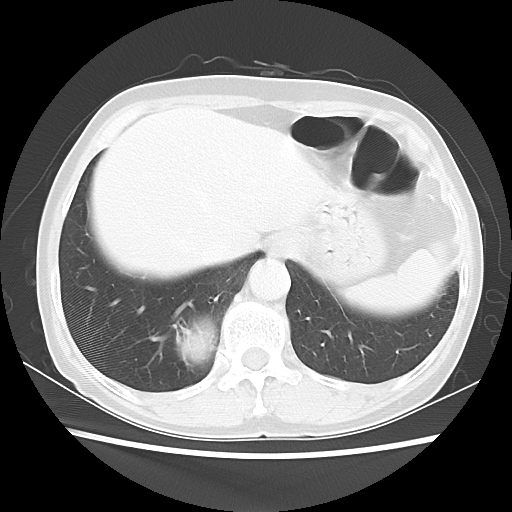
Chest CT, one axial slice; position 9 of 56 along the scan axis; reconstruction kernel LUNG; 120 kVp; lung window (W 1500 / L -600 HU); 5 mm slice thickness; 512 × 512 image matrix, field of view 332 × 332 mm. Patient: female, 66 years. From the clinical record (not read from this slice): clinical TNM (as recorded): T2 N3 M0; histopathological grade: G3.
Outlined on this slice (bounding box drawn by a radiologist):
- lung tumour (recorded histology: small cell carcinoma): bounding box <173,316,221,372> (left, top, right, bottom; pixels)